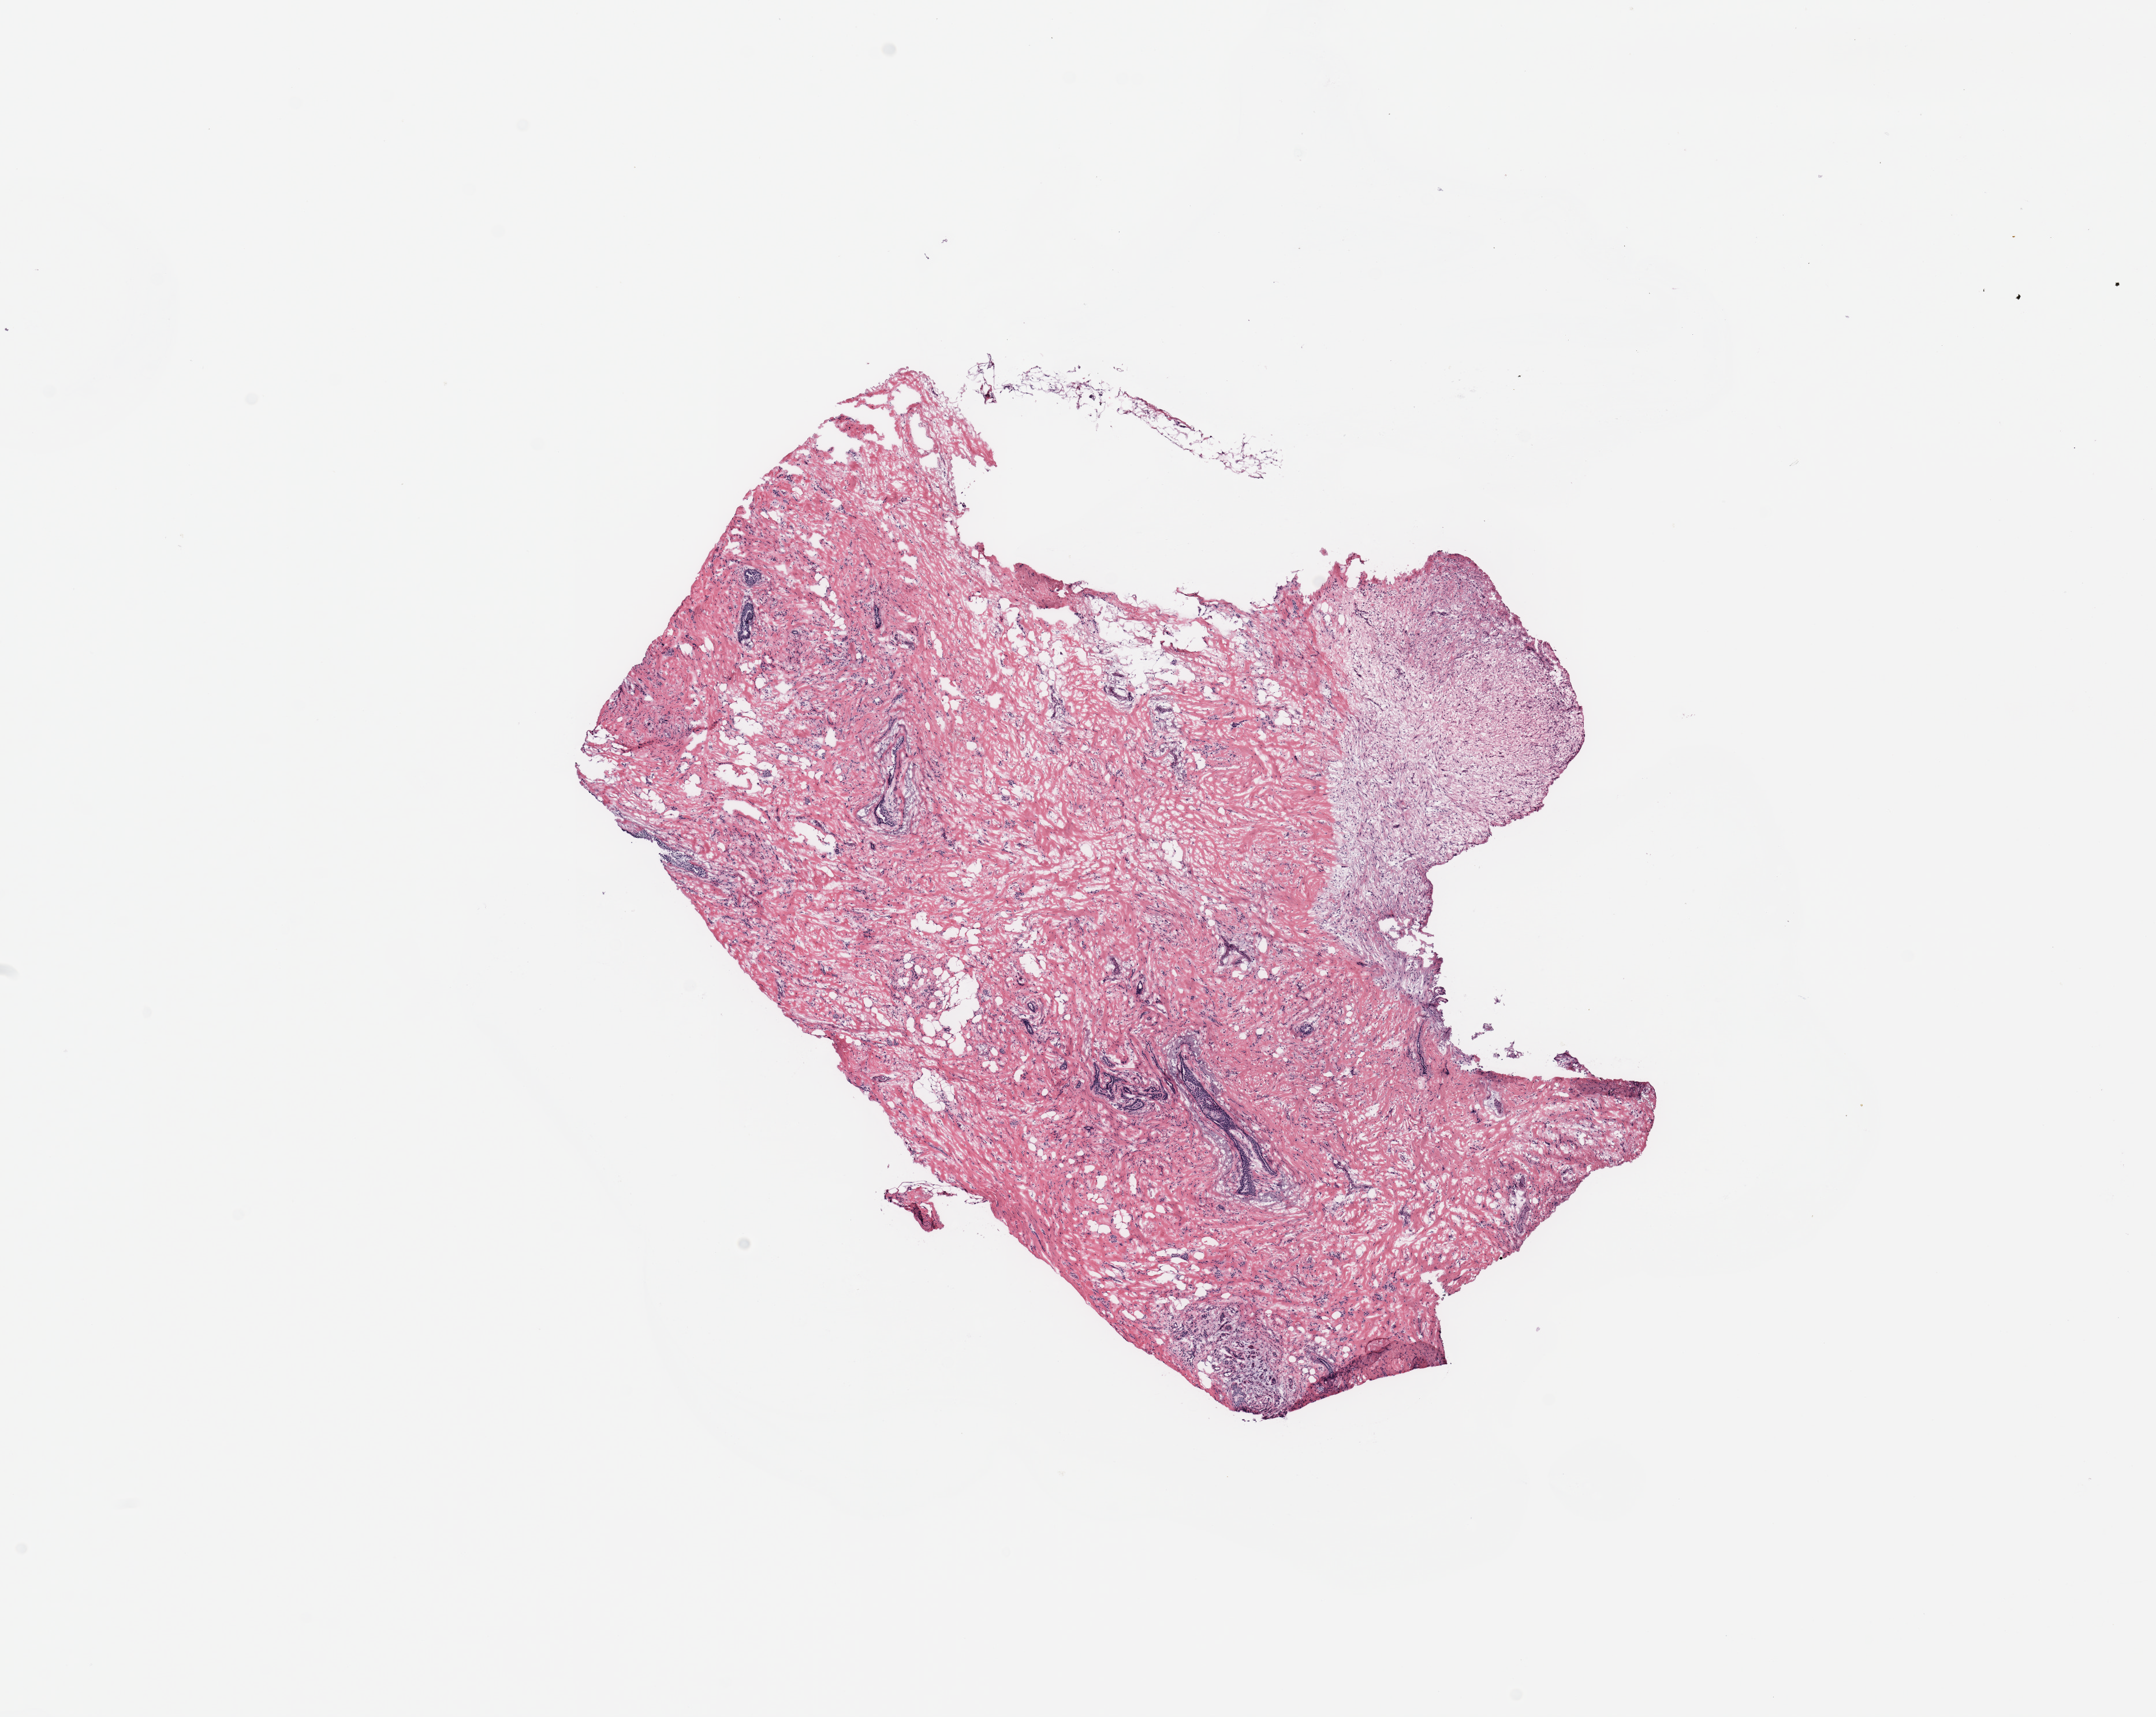
H&E whole-slide image, shown as a low-resolution overview of the whole scanned area (about 14.8 x 11.8 mm, slide scanned at 20x); breast, tissue type not recorded.
Patient diagnosis (cohort enrolment): breast cancer (breast).